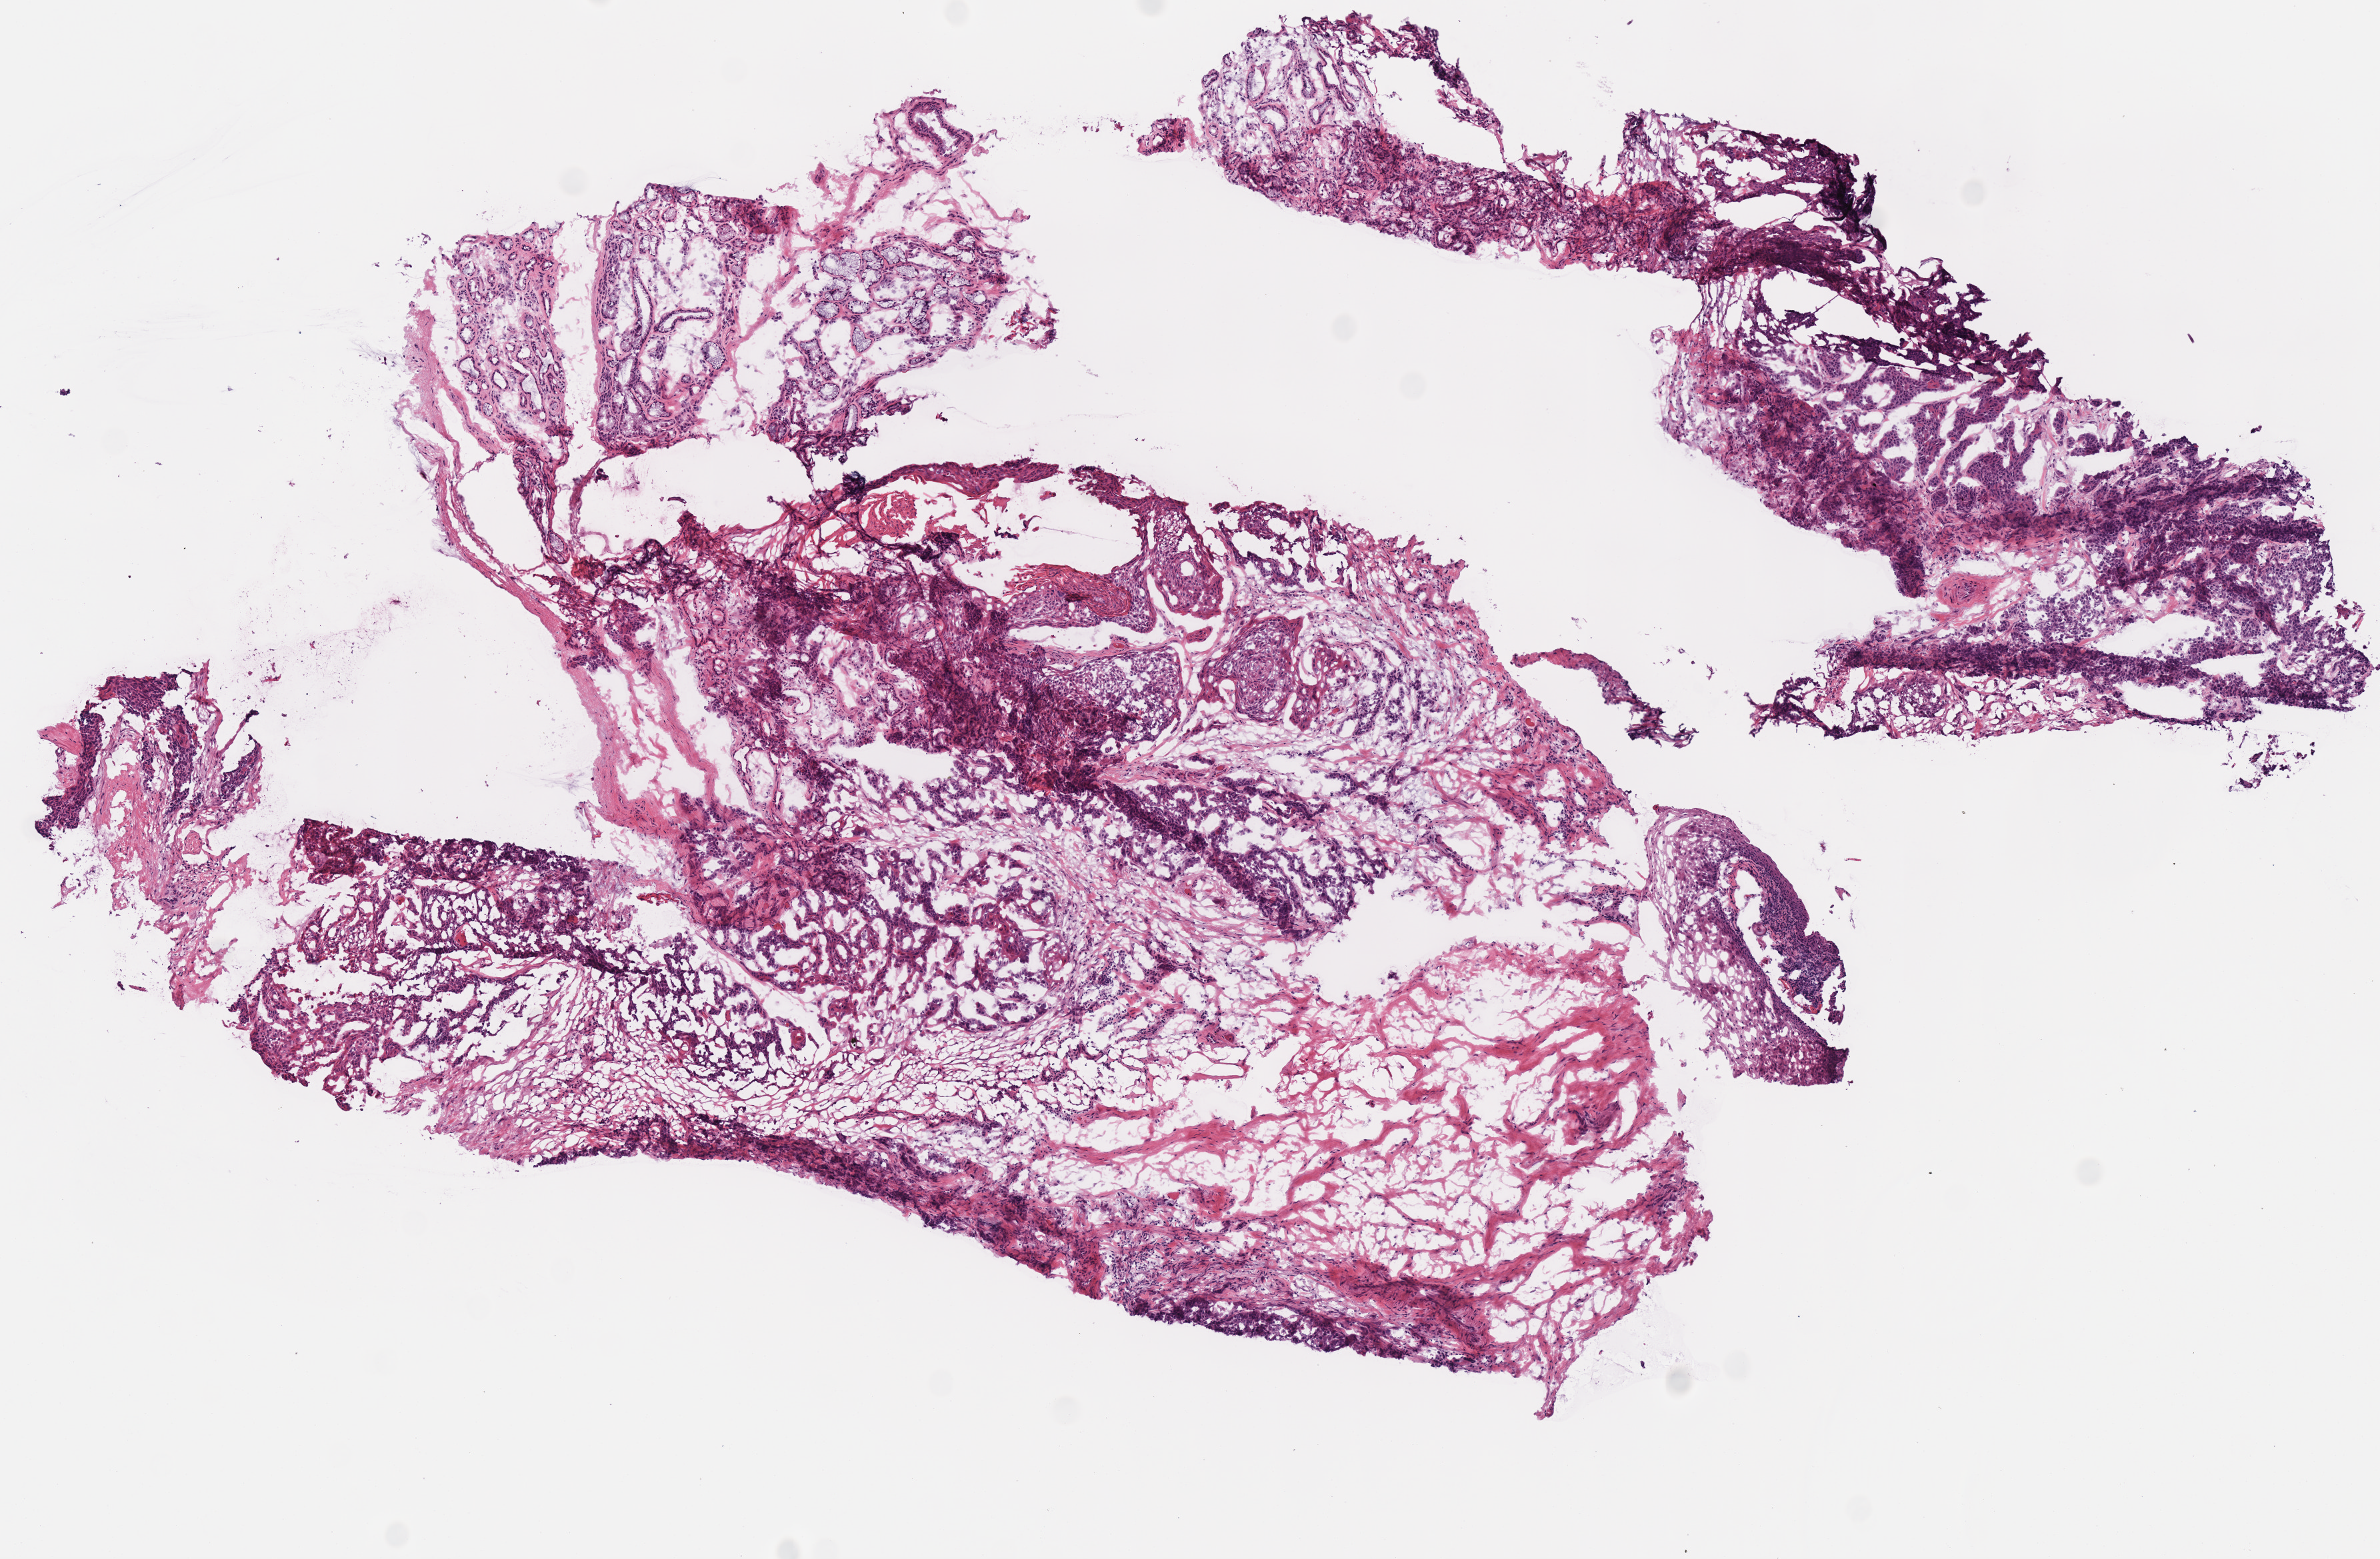
H&E-stained whole-slide image — a low-resolution overview of the entire scanned area, about 7.0 x 4.6 mm. Frozen section. Sample: primary tumour, head and neck. Patient: male, age at initial diagnosis 66 years. Histologic grade: G2 (moderately differentiated). Slide review estimates, as recorded: tumour cells 50%, tumour nuclei 75%, normal cells 10%, stromal cells 40%, necrosis 0%.
AJCC pathologic stage: IVA. Histologic diagnosis: Squamous cell carcinoma, NOS (tongue, NOS).